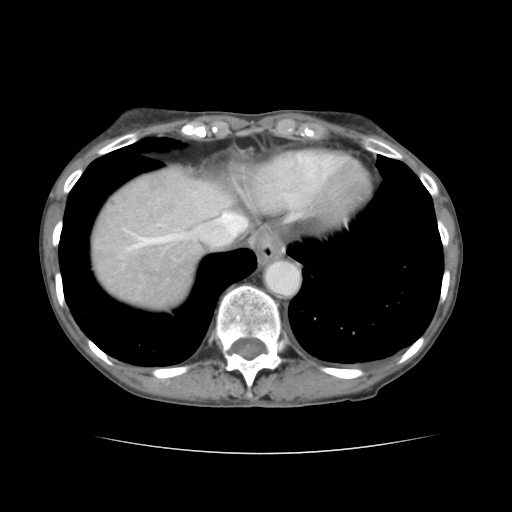
Contrast-enhanced abdominal CT, one axial slice. Slice 126 of 136 in the series (ordered by position). Soft-tissue window (W 400 / L 40 HU). 2.5 mm slice thickness. 512 × 512 image matrix. Female patient, age 77 years. From the clinical record (not read from this slice): diagnosis: colorectal cancer liver metastases, imaged before liver resection; multiple liver metastases: yes; largest metastasis: 3 cm; disease in both lobes: no.
Outlined on this slice (manually delineated by an expert):
- hepatic veins: bounding box [x1, y1, x2, y2] px = [124, 196, 247, 252]
- liver: [91, 167, 234, 309]
- planned liver remnant (the part of the liver to remain after resection): [194, 180, 232, 217]